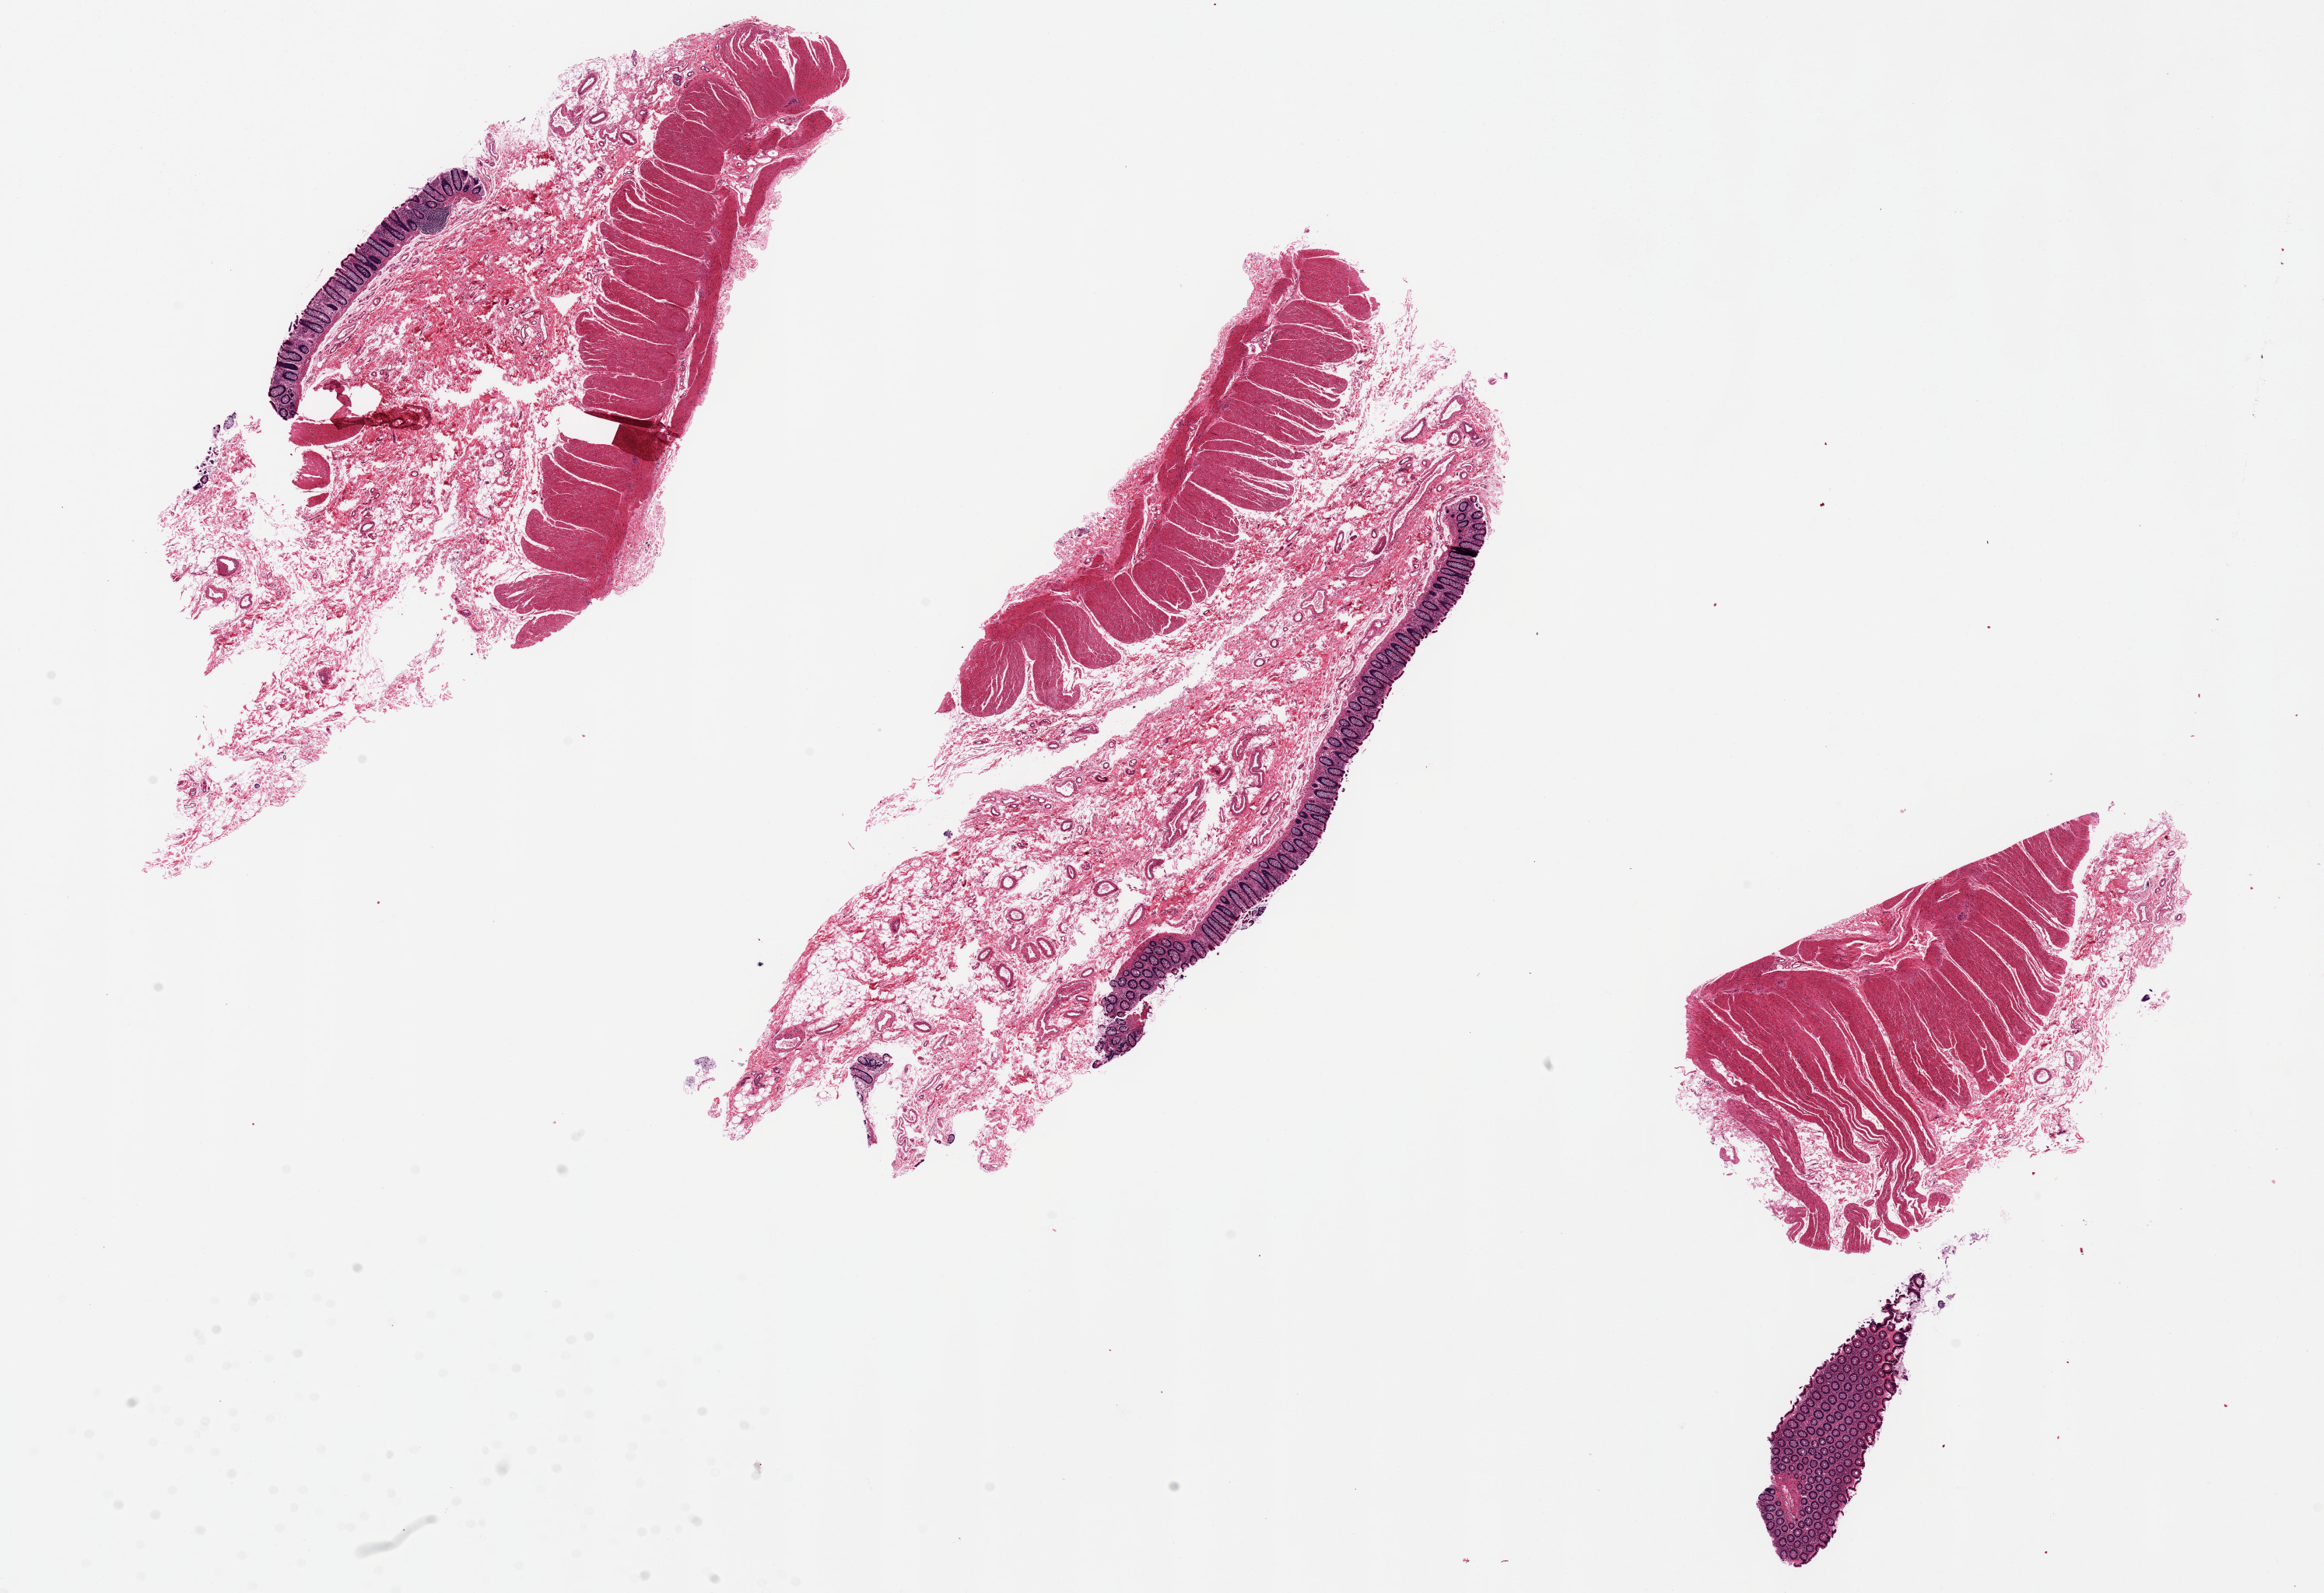
Whole-slide image, haematoxylin and eosin stain — shown as a low-resolution overview of the whole scanned area (about 23.6 x 16.2 mm, acquisition: 20x scan), PAXgene-fixed paraffin-embedded (PFPE) section, target tissue: transverse colon, tissue donor sample. Donor: male.
Review note (as recorded): Well preserved. Mucosa is 10% wall thickness.